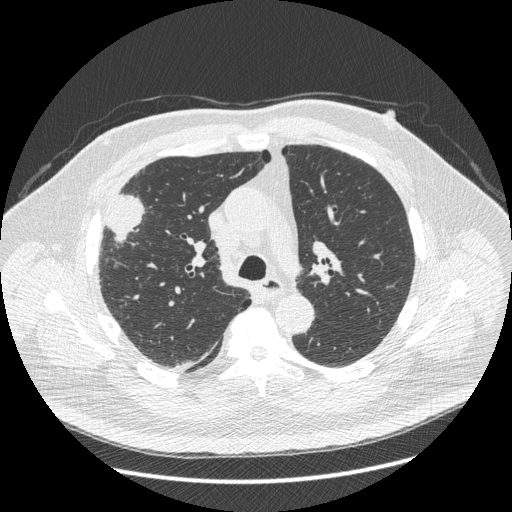
Chest CT (low-dose screening protocol), one axial image, third screening round (two years after baseline), lung window (W 1500 / L -600 HU), 1.25 mm slice thickness, 120 kVp, slice 142 of 426 in the series, 512 × 512 image matrix, field of view 400 × 400 mm. Male, age 66 years at enrolment. Current smoker at enrolment.
Expert-annotated lung lesion, box from (x=86, y=188) to (x=145, y=266) px. Screening reader's record for this exam (one nodule recorded; not confirmed to be the boxed lesion): non-calcified nodule or mass ≥4 mm, right upper lobe, 48 × 25 mm, spiculated (stellate) margins, soft tissue attenuation, pre-existing on the prior screen: no. Participant outcome: lung cancer diagnosed 35 days after this screen — non-small cell carcinoma, right upper lobe, stage IV (AJCC 6th edition), 50 mm at pathology.